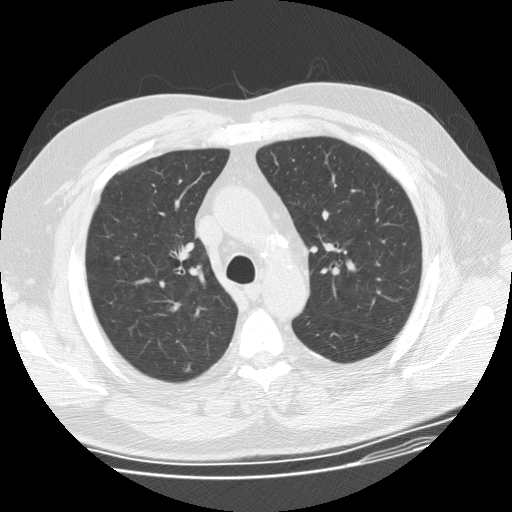
Low-dose screening chest CT, one axial slice. Position 107 of 155 along the scan axis. 120 kVp. Lung window (W 1500 / L -600 HU). 2.5 mm slice thickness. 512 × 512 image matrix.
Annotated regions visible in this slice (outlined manually by an expert reader):
- lesion 1 (tumor, upper lobe of right lung): bounding box [x1, y1, x2, y2] px = [182, 362, 191, 372]